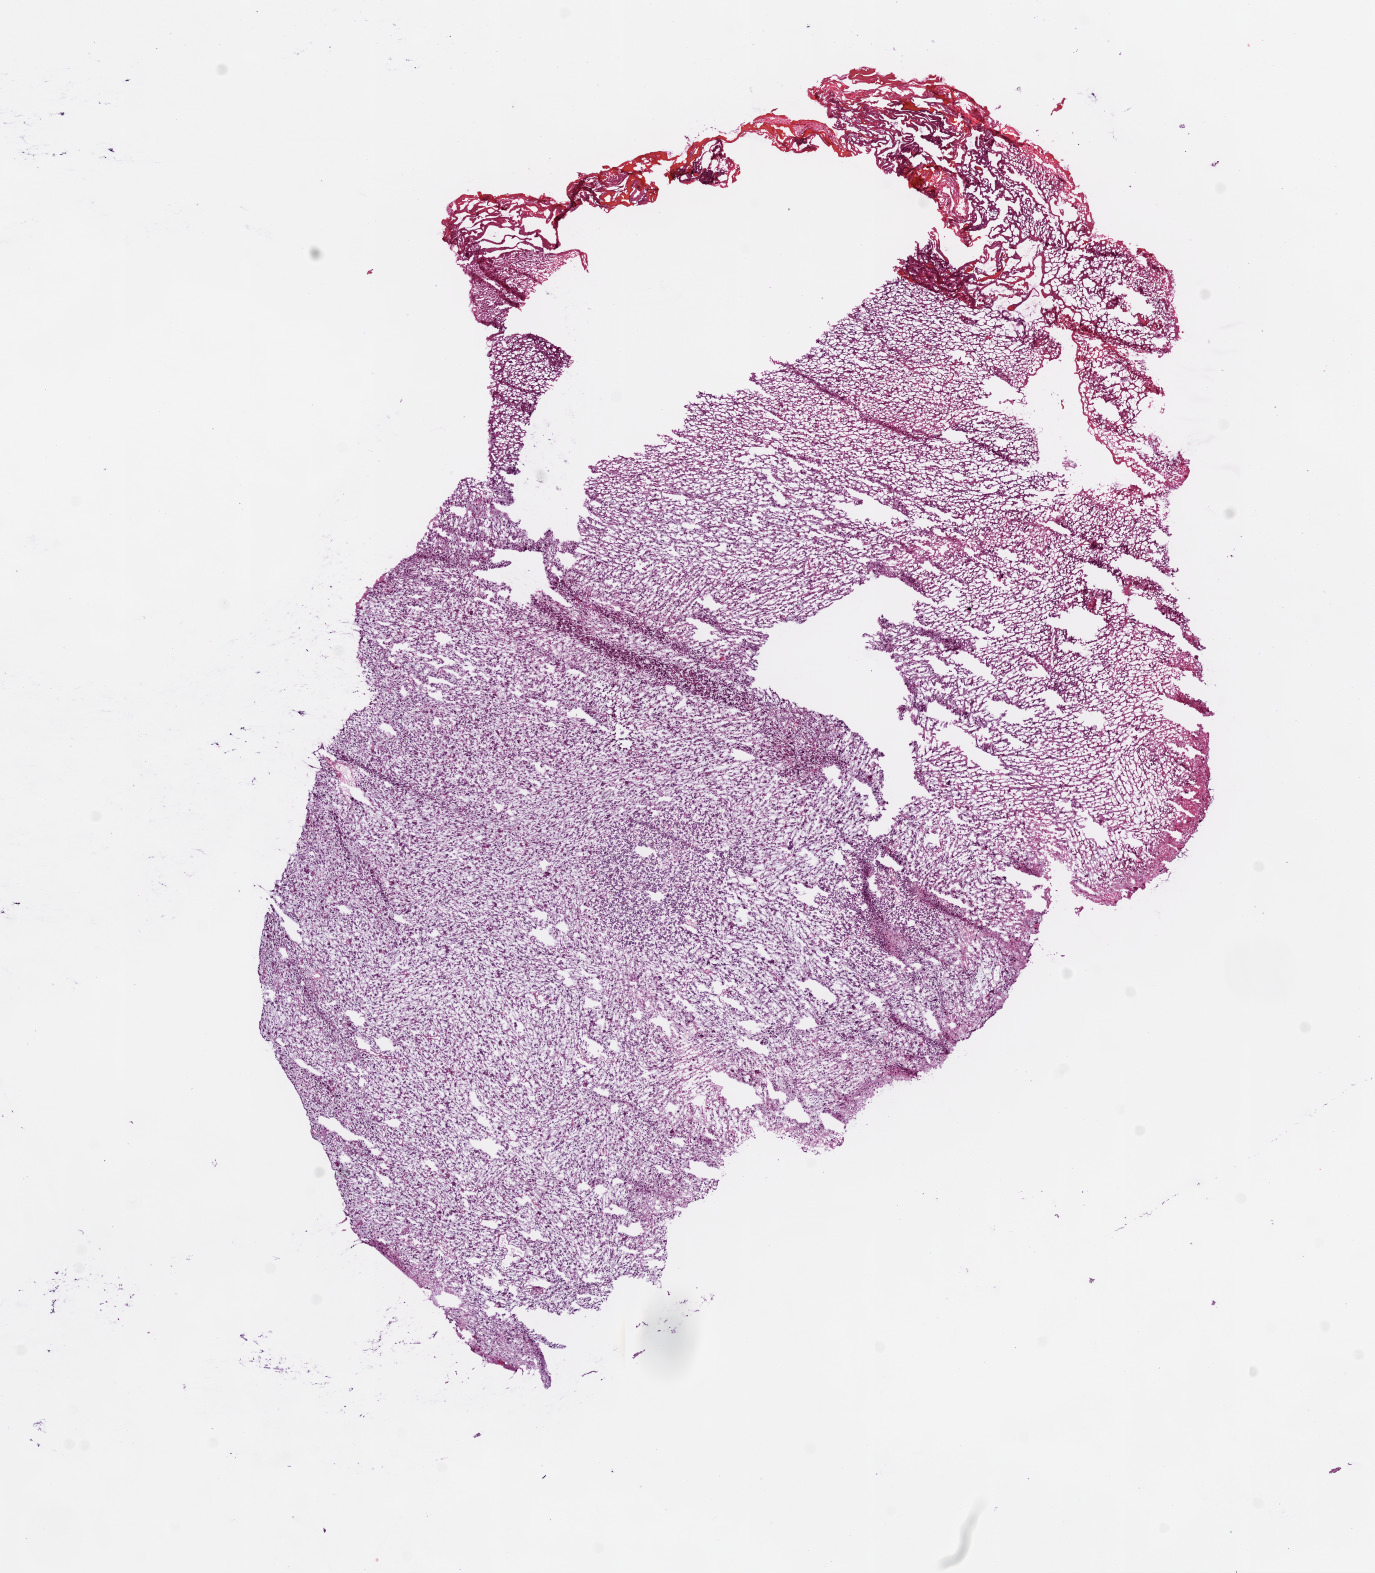
Whole-slide histology image, H&E-stained — a low-resolution overview of the entire scanned area, about 11.0 x 12.6 mm (from a 20x scan). Frozen section from the bottom of the tissue portion. Primary tumour sample from the brain. Female, age 59 years at initial diagnosis. Slide review estimates, as recorded: tumour cells 75%, tumour nuclei 85%, normal cells 0%, stromal cells 5%, necrosis 20%.
Diagnosis: Glioblastoma.